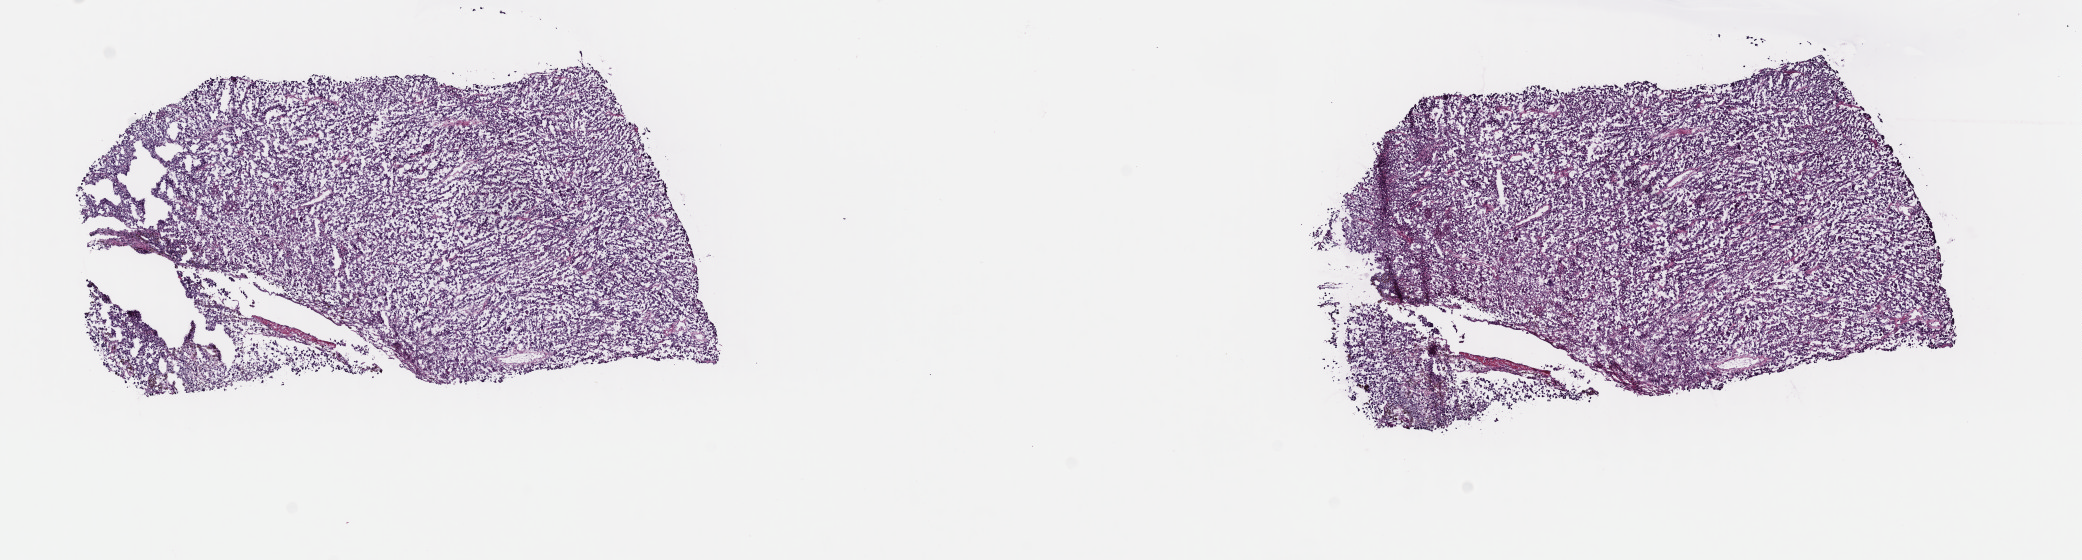
Whole-slide histology image, Hematoxylin and eosin (H&E) stained — shown as a low-resolution overview of the whole scanned area (about 16.4 x 4.4 mm, from a 40x scan). Frozen section from the top of the tissue portion. Metastatic tumour sample. Male patient; age at initial diagnosis 55 years. Pathologist review of this section (percent, as recorded): tumour cells 85%, tumour nuclei 85%, normal cells 0%, stromal cells 15%, necrosis 0%. Infiltration values recorded for this section: lymphocyte infiltration 2%, monocyte infiltration 0%, neutrophil infiltration 0%.
- this section: metastatic tumour tissue
- patient diagnosis: Malignant melanoma, NOS